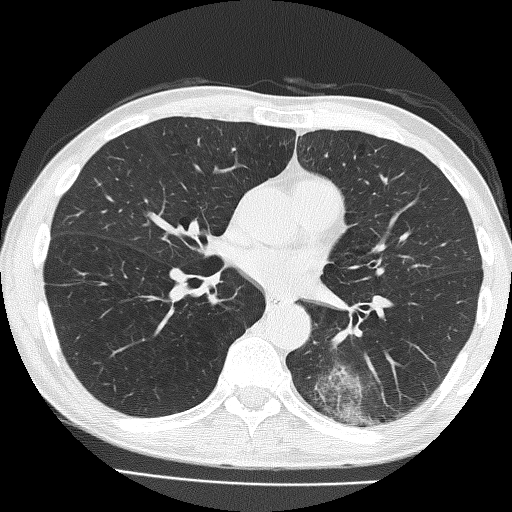
Low-dose screening chest CT, one axial slice; position 79 of 160 along the scan axis; lung window (W 1500 / L -600 HU); 2 mm slice thickness; 512 × 512 image matrix, field of view 324 × 324 mm.
Outlined on this slice (manually delineated by an expert):
- lesion 1 (tumor, lower lobe of left lung): bounding box <332,331,347,346> (left, top, right, bottom; pixels)